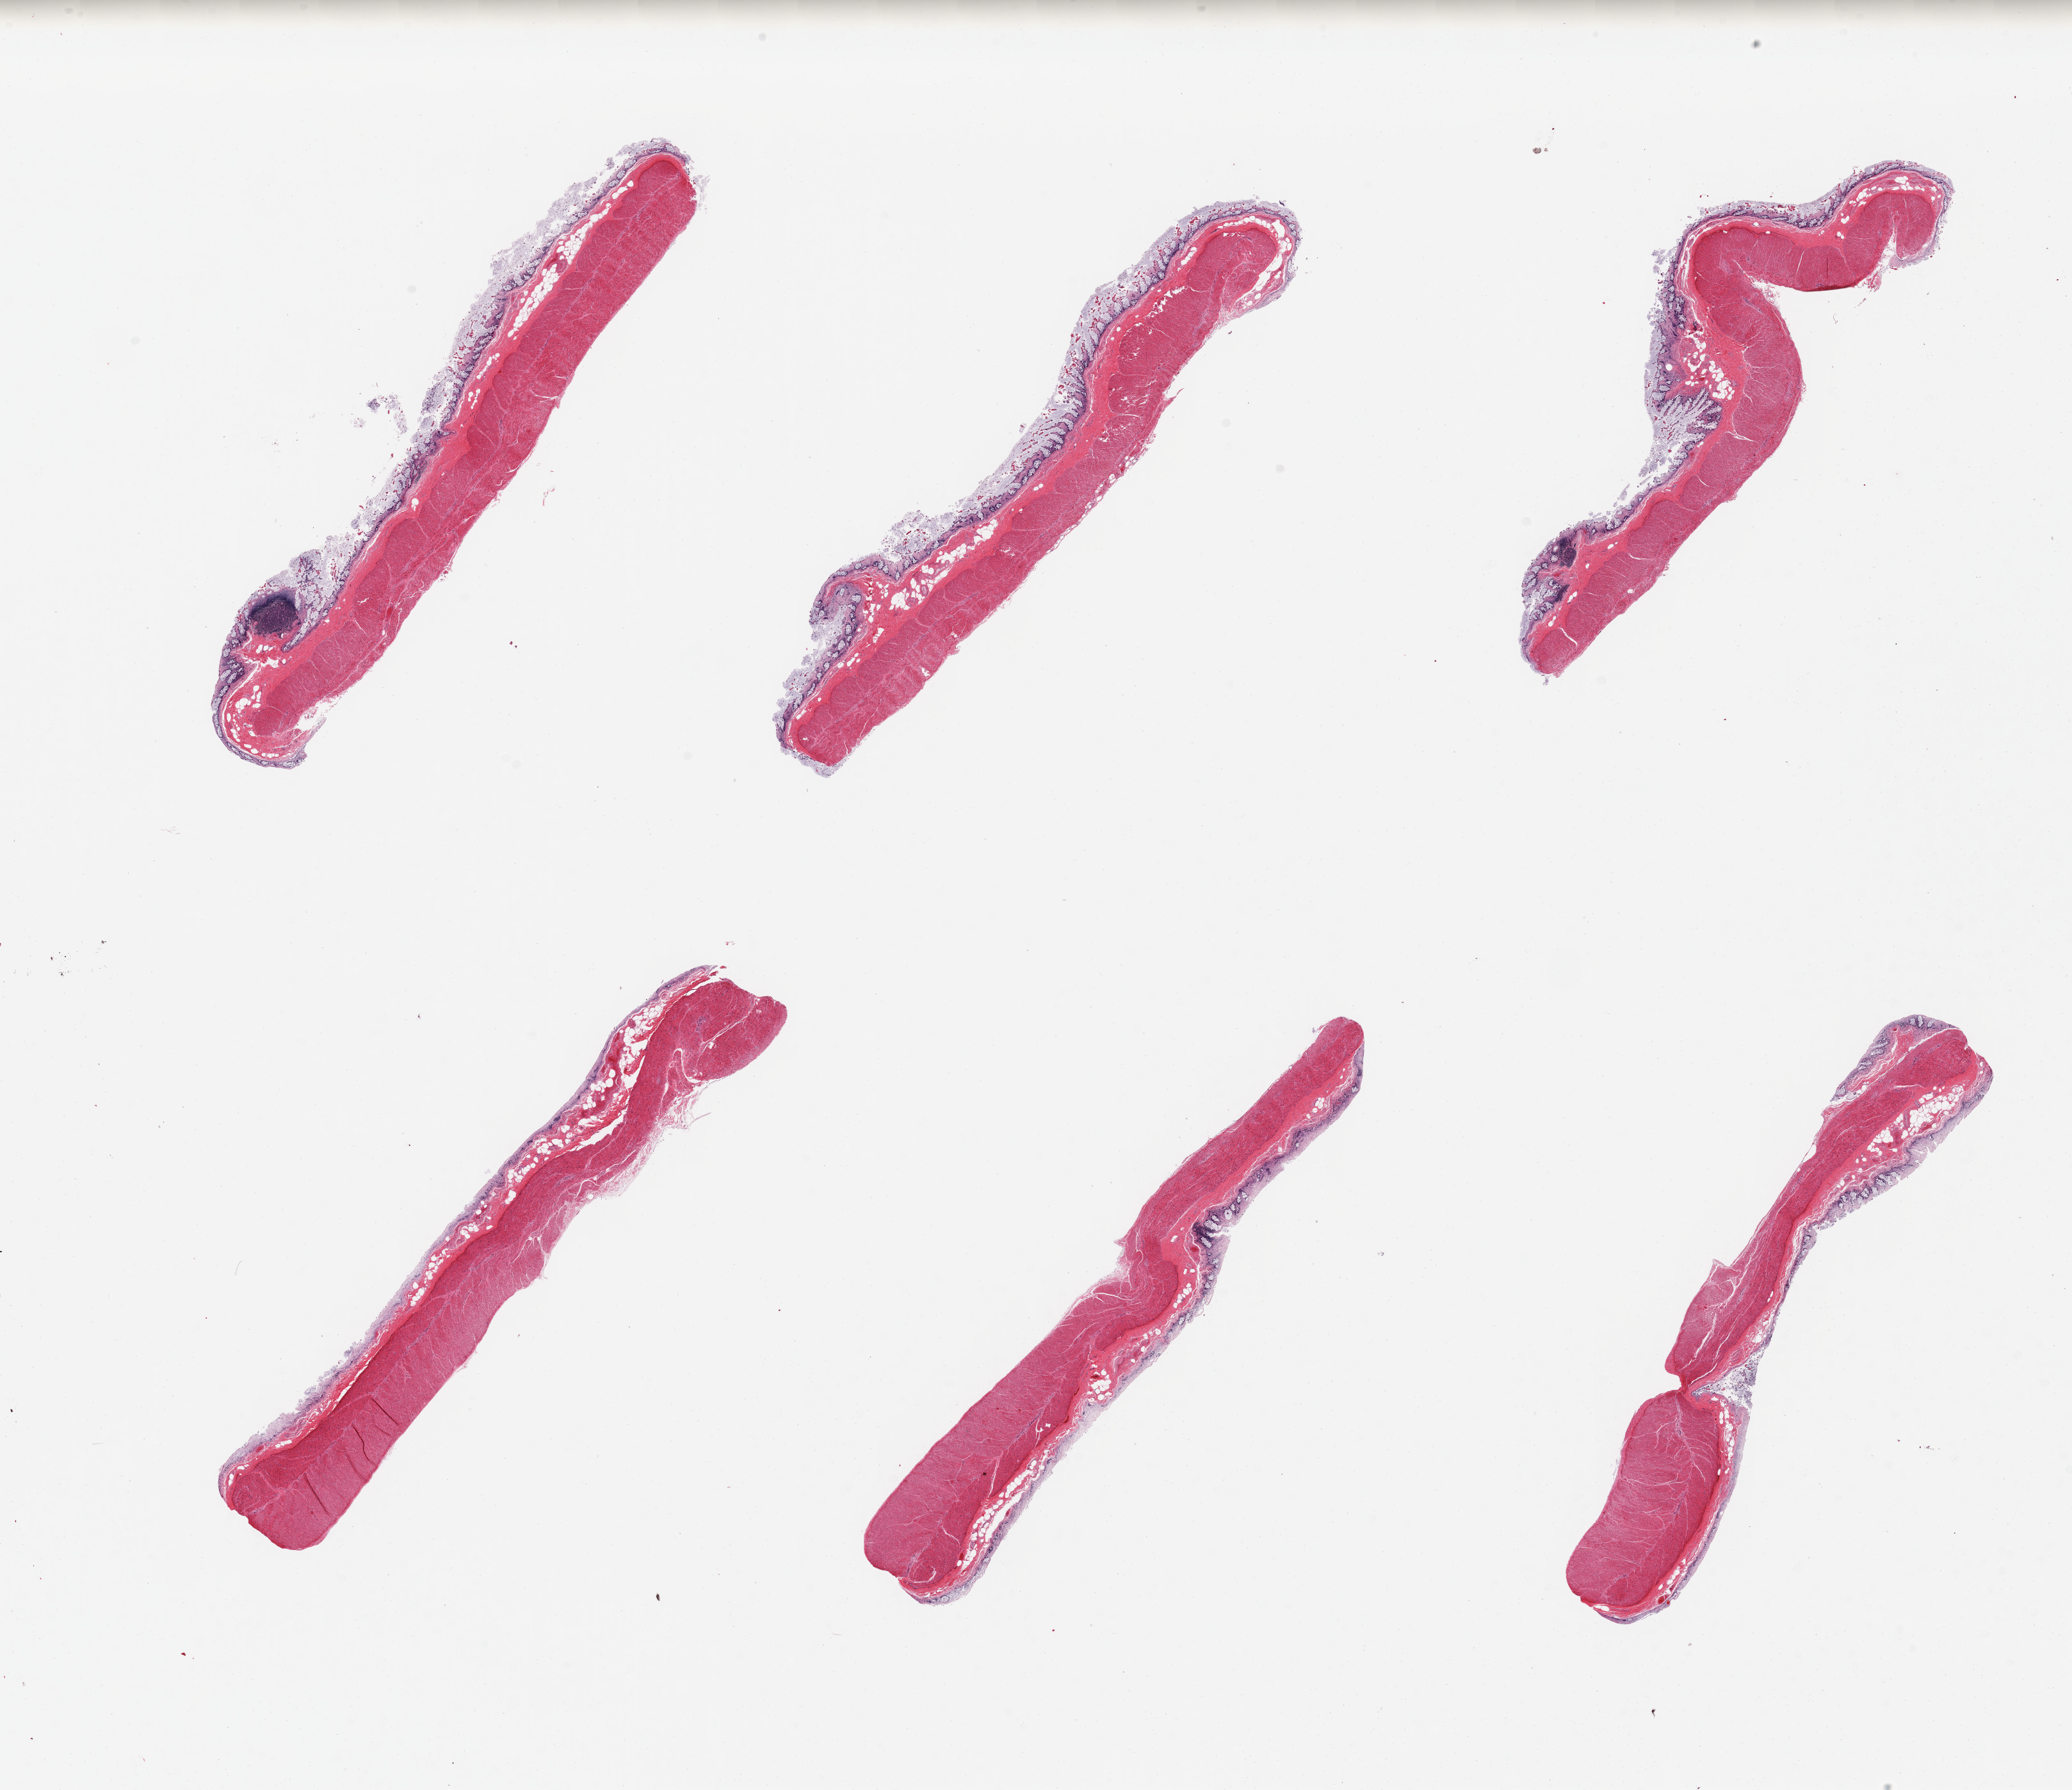
Haematoxylin and eosin whole-slide image, brightfield — low-resolution overview of the scanned area, about 25.6 x 22.1 mm; PAXgene-fixed paraffin-embedded (PFPE) section; target tissue: transverse colon; tissue donor sample. Donor: male.
- reviewer comment on this tissue sample: 6 pieces, mucosa toally autoyzed and/or sloughed